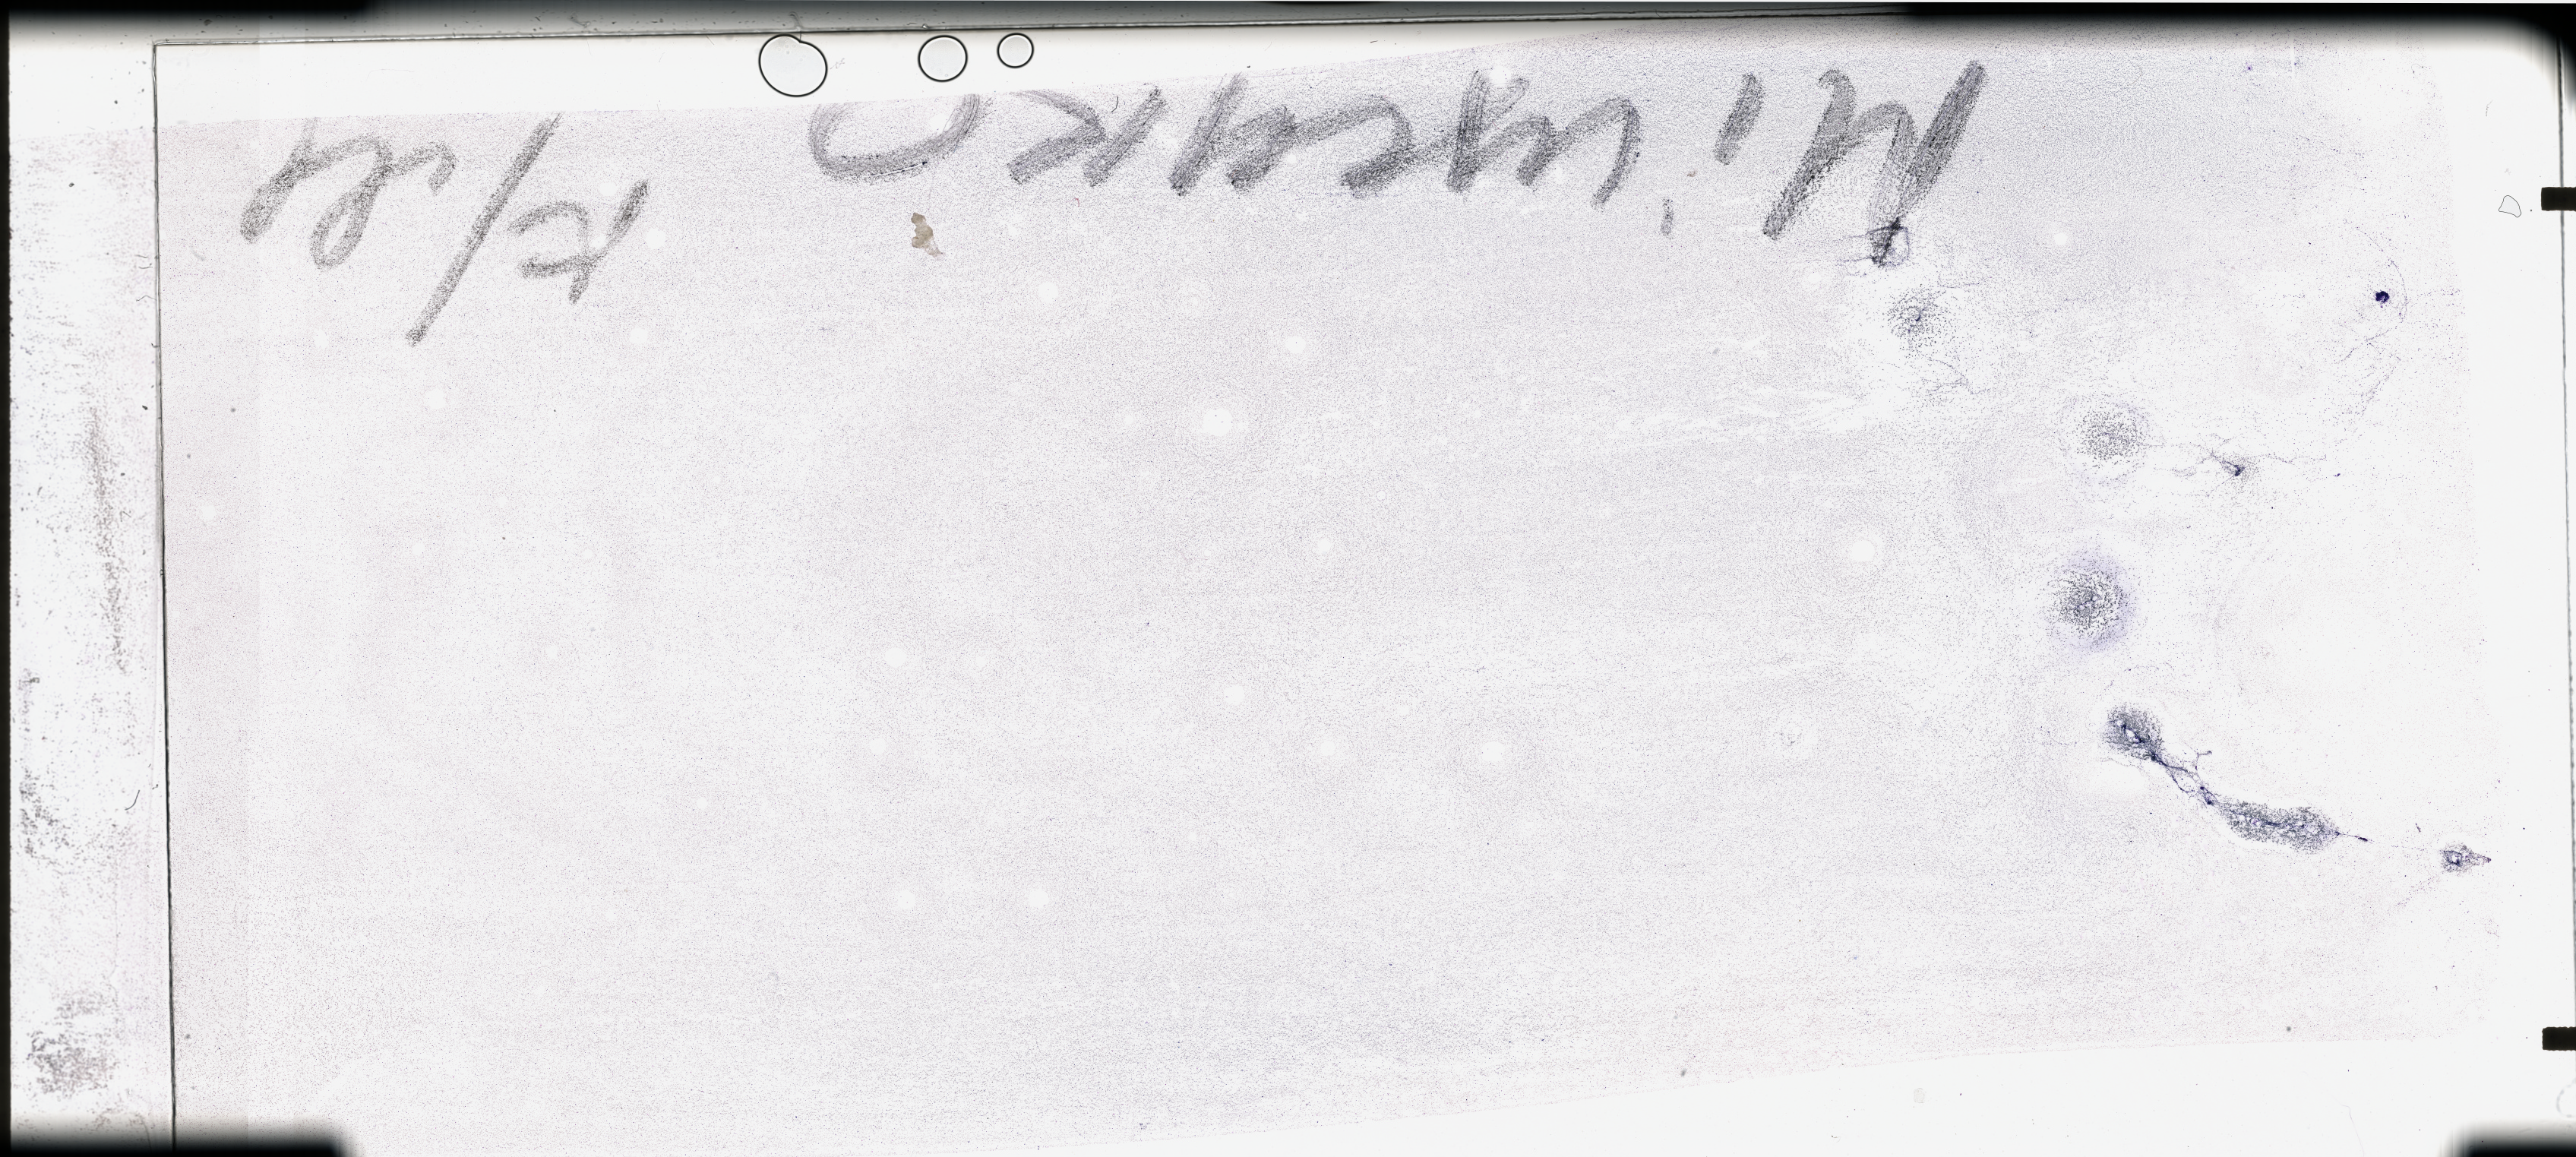
H&E whole-slide image — whole scanned area (about 53.5 x 24.0 mm) shown as a low-resolution overview; bone marrow (leukaemic) sample. 45-year-old male patient. Blasts: 10%.
- diagnosis: Acute Myeloid Leukemia
- FAB classification: M4